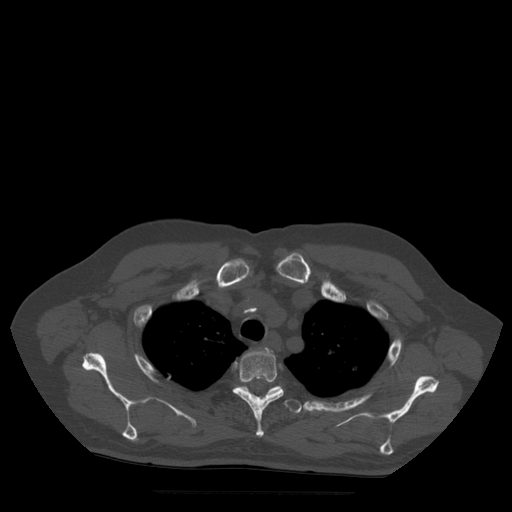
CT including the spine, one axial slice; slice 406 of 522 in the series (ordered by position); bone window (W 1800 / L 400 HU); 1.25 mm slice thickness; 512 × 512 image matrix, field of view 420 × 420 mm. Patient age 72 years. From the clinical record (not read from this slice): primary cancer: prostate.
Annotated regions visible in this slice (semi-automatic segmentation, software-assisted and operator-edited):
- T3 vertebra: box from (x=233, y=348) to (x=284, y=437) px
- T4 vertebra: (x=238, y=386)–(x=302, y=414)